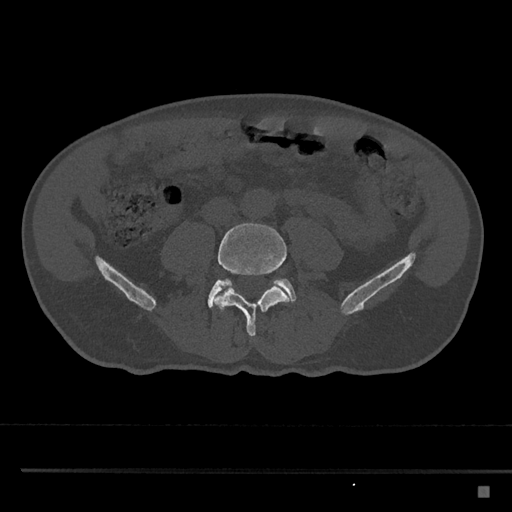
CT including the spine, one axial slice; slice 620 of 797 in the series (ordered by position); bone window (W 1800 / L 400 HU); 0.5 mm slice thickness; 512 × 512 image matrix, field of view 391 × 391 mm. Patient: male, 59 years. From the clinical record (not read from this slice): primary cancer: prostate.
Outlined on this slice (semi-automatic segmentation, software-assisted and operator-edited):
- L4 vertebra: bounding box [x1, y1, x2, y2] px = [215, 223, 291, 337]
- L5 vertebra: [208, 278, 296, 310]